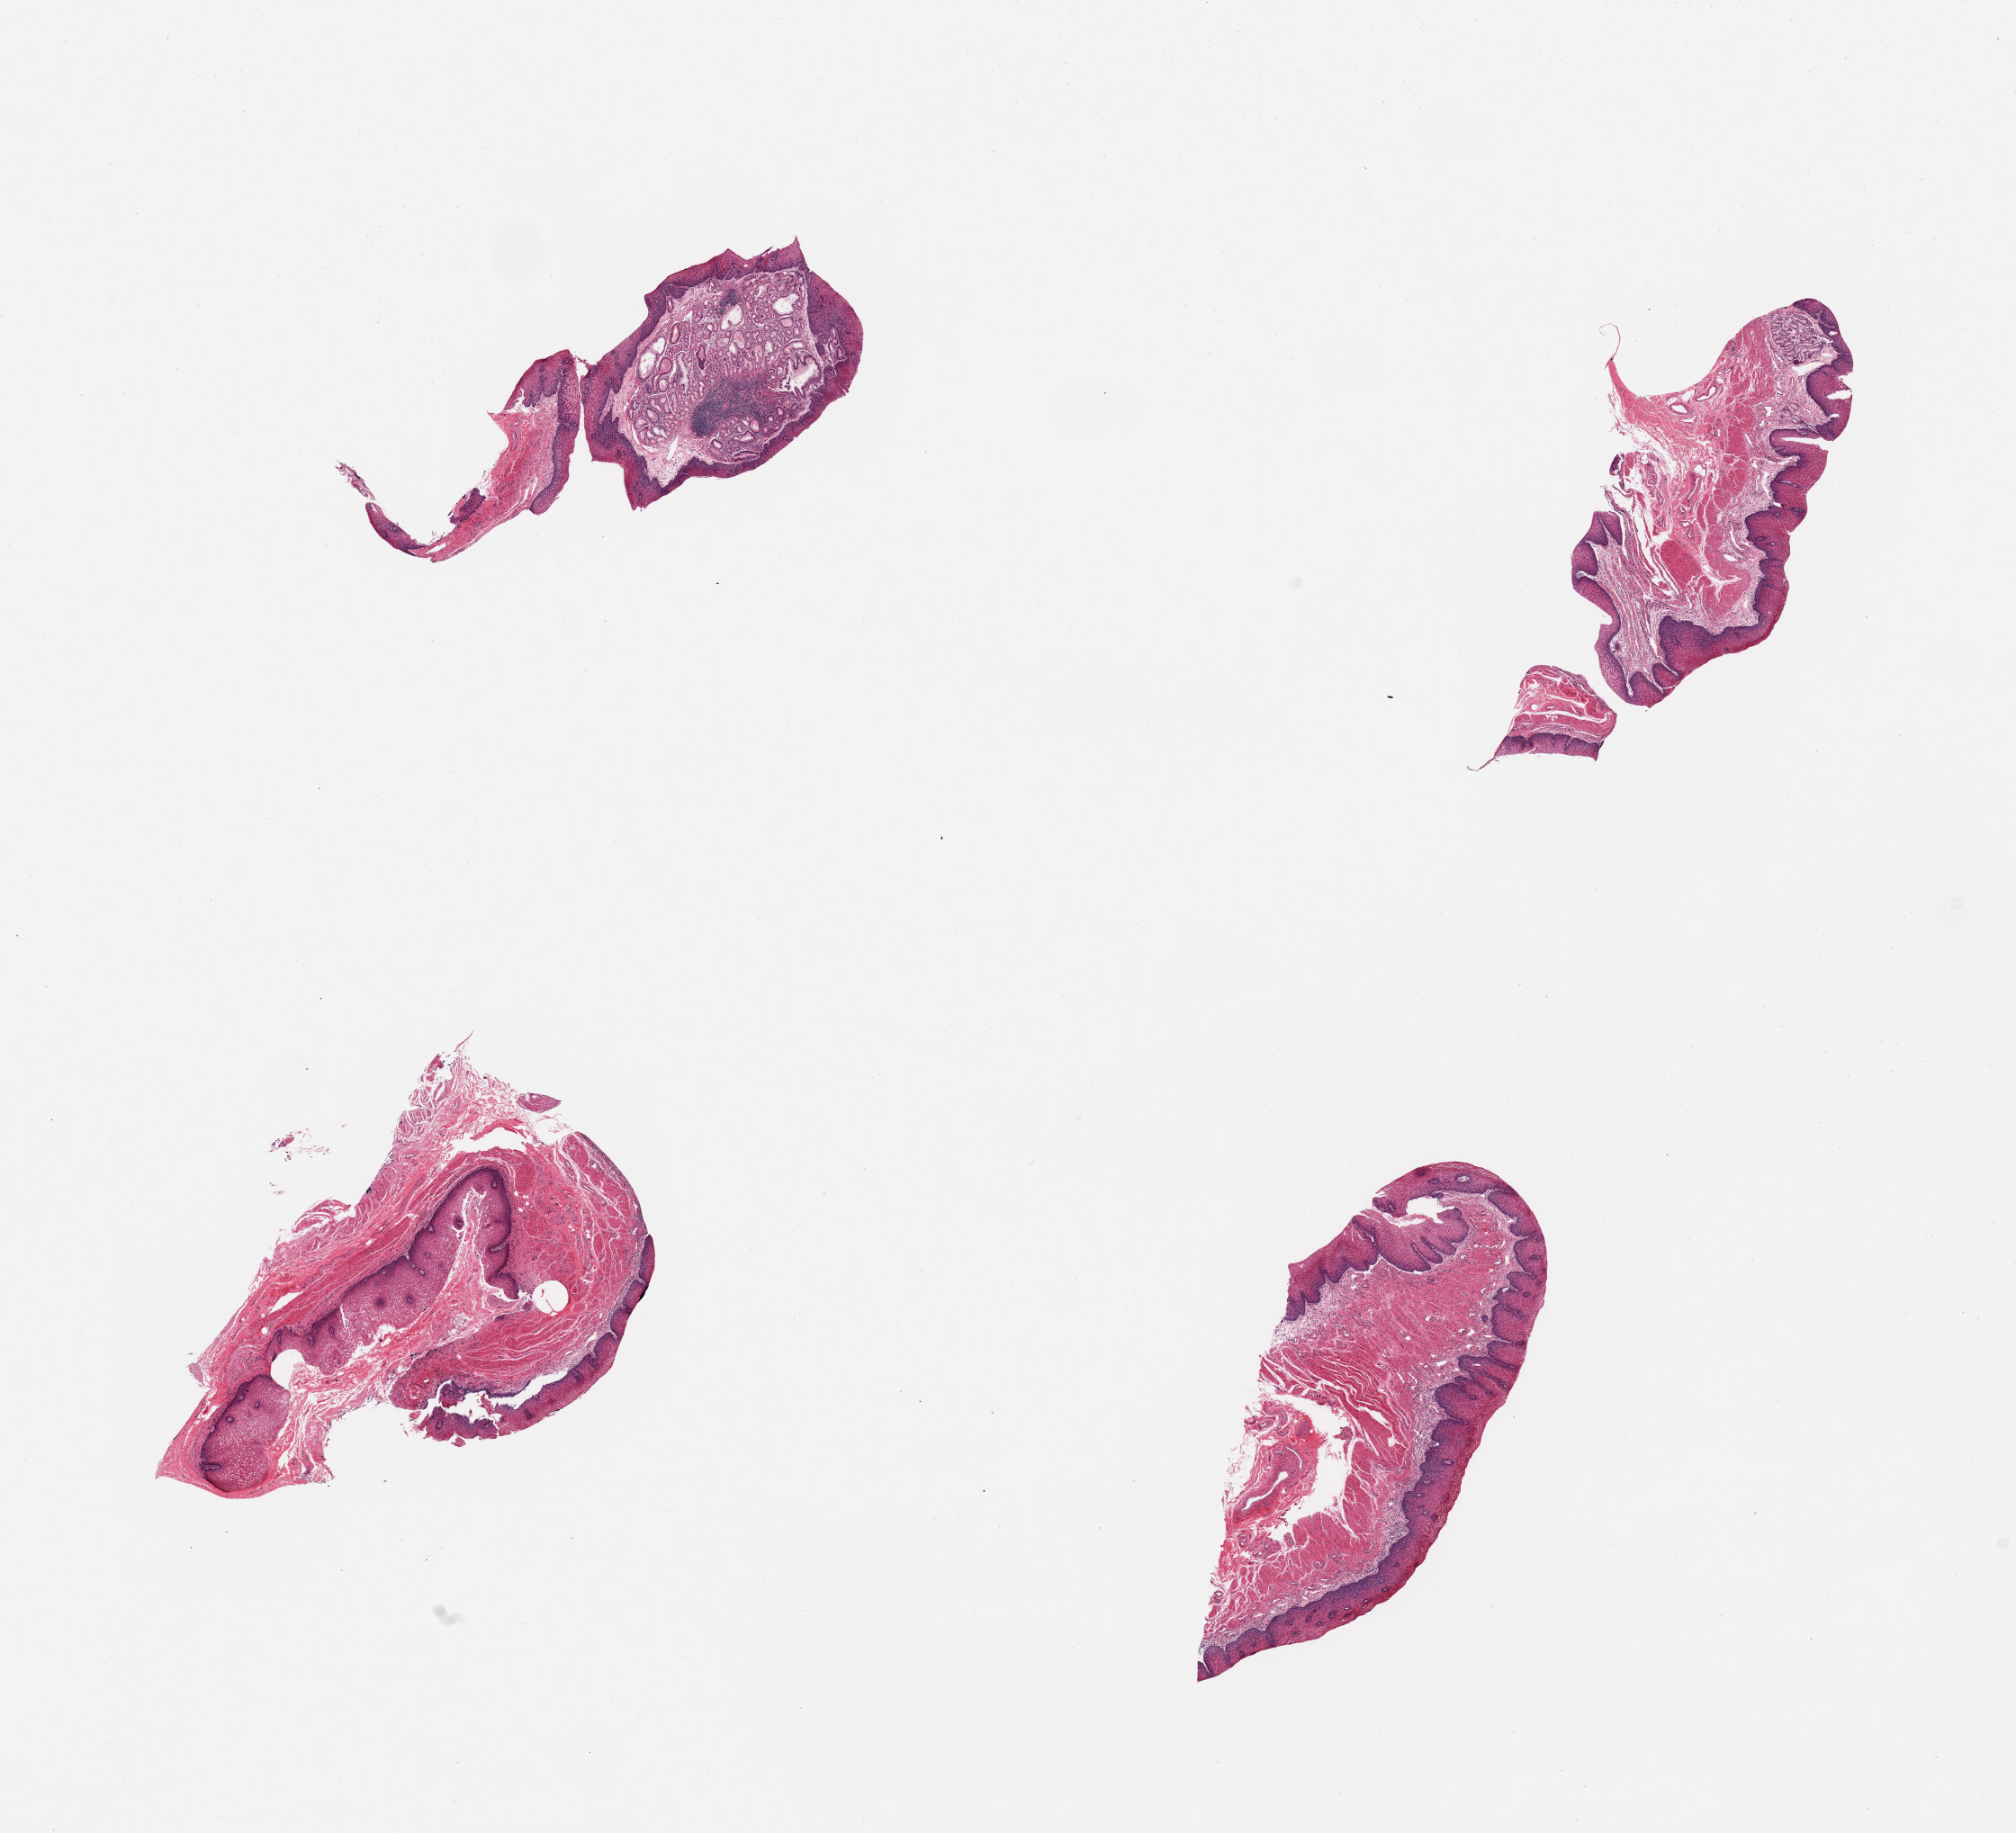
Haematoxylin and eosin whole-slide image — shown as a low-resolution overview of the whole scanned area (about 17.7 x 16.1 mm, acquisition: 20x scan). PAXgene-fixed, paraffin-embedded tissue. Sampled site (target tissue): gastroesophageal junction. Tissue donor sample. Donor: female.
Review note (as recorded): 4 pieces; mucosa, not muscularis (target).